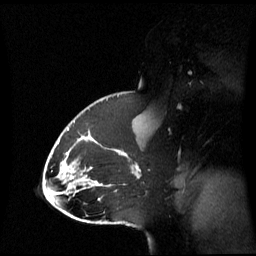
Breast MRI (dynamic contrast-enhanced), one sagittal slice. Slice 40 of 60 in the series (ordered by position). Dynamic contrast-enhanced series, image 2 of 3 at this slice position (ordered by acquisition). 1.5 T. TE 4.2 ms, TR 8.4 ms. 2.8 mm slice thickness. 256 × 256 image matrix, field of view 270 × 270 mm. Patient: female, 43 years. Case-level facts recorded for this patient, not image findings: setting: breast cancer imaged before/during neoadjuvant chemotherapy; receptor status: triple-negative.
Outlined on this slice (semi-automatic segmentation, software-assisted and operator-edited):
- analysis volume of interest (the breast-tissue region the enhancement analysis was run in; not a lesion): bounding box (x1, y1, x2, y2) in pixels: (65, 118, 143, 198)
- tumour enhancement mask (voxels above the 70 % enhancement threshold inside the analysis volume of interest): (67, 128, 119, 152)